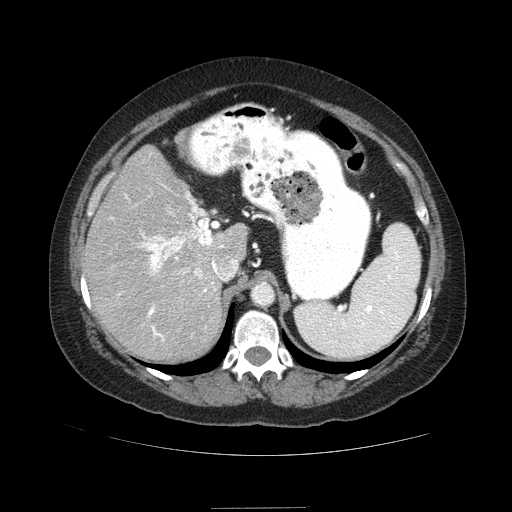
Contrast-enhanced abdominal CT (liver protocol), one axial slice; slice 57 of 89 in the series (ordered by position); reconstruction kernel STANDARD; 120 kVp; soft-tissue window (W 400 / L 40 HU); 512 × 512 image matrix. From the clinical record (not read from this slice): diagnosis: hepatocellular carcinoma (patient treated with transarterial chemoembolisation; whether this scan precedes or follows treatment is not stated here); TNM stage (as recorded): Stage-IIIB; Child-Pugh class: A; tumour nodularity: multinodular.
Structures marked on this image (semi-automatically segmented with operator editing):
- abdominal aorta: bounding box [x1, y1, x2, y2] px = [253, 283, 272, 304]
- liver parenchyma outside the tumour (the mass and vessels are separate outlines, so this box may not span the whole liver): [82, 146, 248, 362]
- liver vessels: [111, 193, 224, 341]